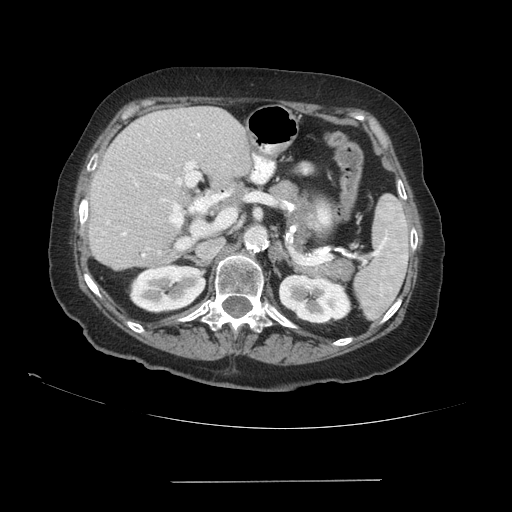
Contrast-enhanced abdominal CT (liver protocol), one axial slice; slice 54 of 89 in the series (ordered by position); 140 kVp; soft-tissue window (W 400 / L 40 HU); 2.5 mm slice thickness; 512 × 512 image matrix, field of view 400 × 400 mm. From the clinical record (not read from this slice): diagnosis: hepatocellular carcinoma (patient treated with transarterial chemoembolisation; whether this scan precedes or follows treatment is not stated here); TNM stage (as recorded): Stage-IVA; Child-Pugh class: A; tumour nodularity: uninodular.
Annotated regions visible in this slice (semi-automatic segmentation, software-assisted and operator-edited):
- liver parenchyma outside the tumour (the mass and vessels are separate outlines, so this box may not span the whole liver): box from (x=88, y=106) to (x=252, y=268) px
- liver vessels: (x=107, y=133)–(x=232, y=257)